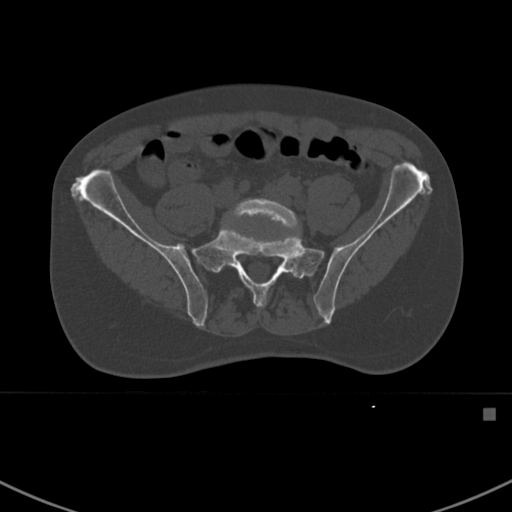
CT including the spine, one axial slice; position 206 of 412 along the scan axis; reconstruction kernel Br40s; 120 kVp; bone window (W 1800 / L 400 HU); 1.5 mm slice thickness; 512 × 512 image matrix, field of view 358 × 358 mm. Male patient, age 59 years. From the clinical record (not read from this slice): primary cancer: prostate.
Outlined on this slice (semi-automatically segmented with operator editing):
- L5 vertebra: bounding box <227,198,299,232> (left, top, right, bottom; pixels)